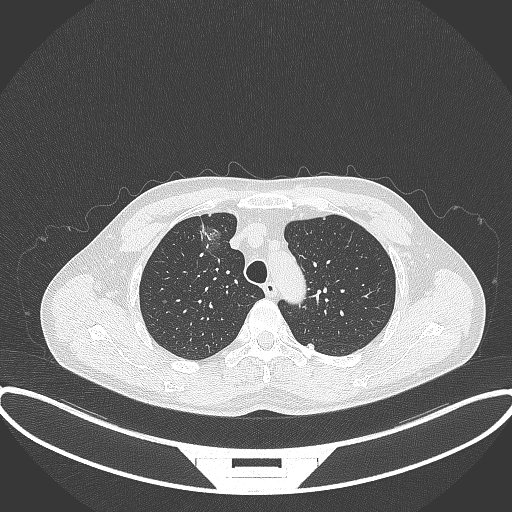
Chest CT, one axial slice; slice 284 of 395 in the series (ordered by position); lung window (W 1500 / L -600 HU); 1 mm slice thickness; 512 × 512 image matrix. Patient: male, 60 years. Case-level facts recorded for this patient, not image findings: clinical TNM (as recorded): T1c N0 M0.
Structures marked on this image (rectangle marked by the reading radiologist):
- lung tumour (recorded histology: adenocarcinoma): bounding box [x1, y1, x2, y2] px = [194, 217, 225, 256]